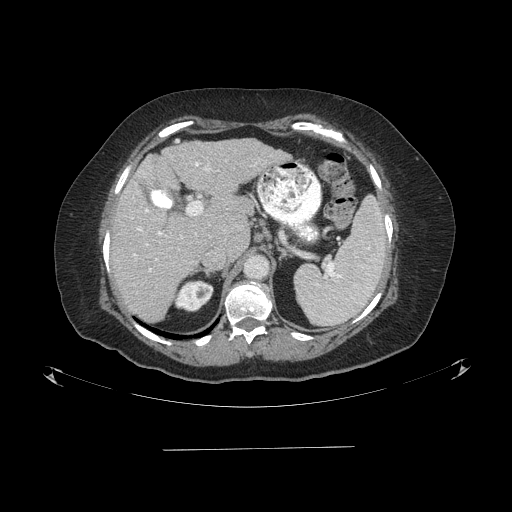
Contrast-enhanced abdominal CT (liver protocol), one axial slice. Slice 54 of 103 in the series (ordered by position). Reconstruction kernel STANDARD. One of 2 acquisitions stored at this slice position. Soft-tissue window (W 400 / L 40 HU). 2.5 mm slice thickness. 512 × 512 image matrix, field of view 500 × 500 mm. Case-level facts recorded for this patient, not image findings: diagnosis: hepatocellular carcinoma (patient treated with transarterial chemoembolisation; whether this scan precedes or follows treatment is not stated here); TNM stage (as recorded): Stage-IIIA; Child-Pugh class: A; tumour nodularity: multinodular.
Structures marked on this image (semi-automatic segmentation, software-assisted and operator-edited):
- liver parenchyma outside the tumour (the mass and vessels are separate outlines, so this box may not span the whole liver): box from (x=110, y=138) to (x=288, y=322) px
- liver vessels: (x=133, y=162)–(x=211, y=271)